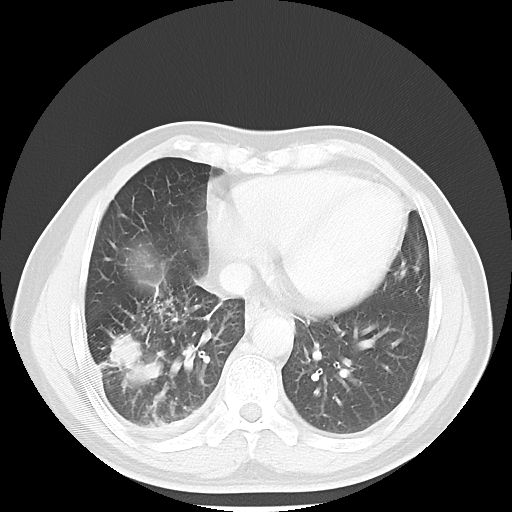
Chest CT, one axial slice; slice 19 of 56 in the series (ordered by position); 120 kVp; lung window (W 1500 / L -600 HU); 5 mm slice thickness; 512 × 512 image matrix, field of view 344 × 344 mm. Patient: male, 56 years. From the clinical record (not read from this slice): clinical TNM (as recorded): T2 N3 M1.
Annotated regions visible in this slice (rectangle marked by the reading radiologist):
- lung tumour (recorded histology: adenocarcinoma): bounding box <108,326,163,390> (left, top, right, bottom; pixels)